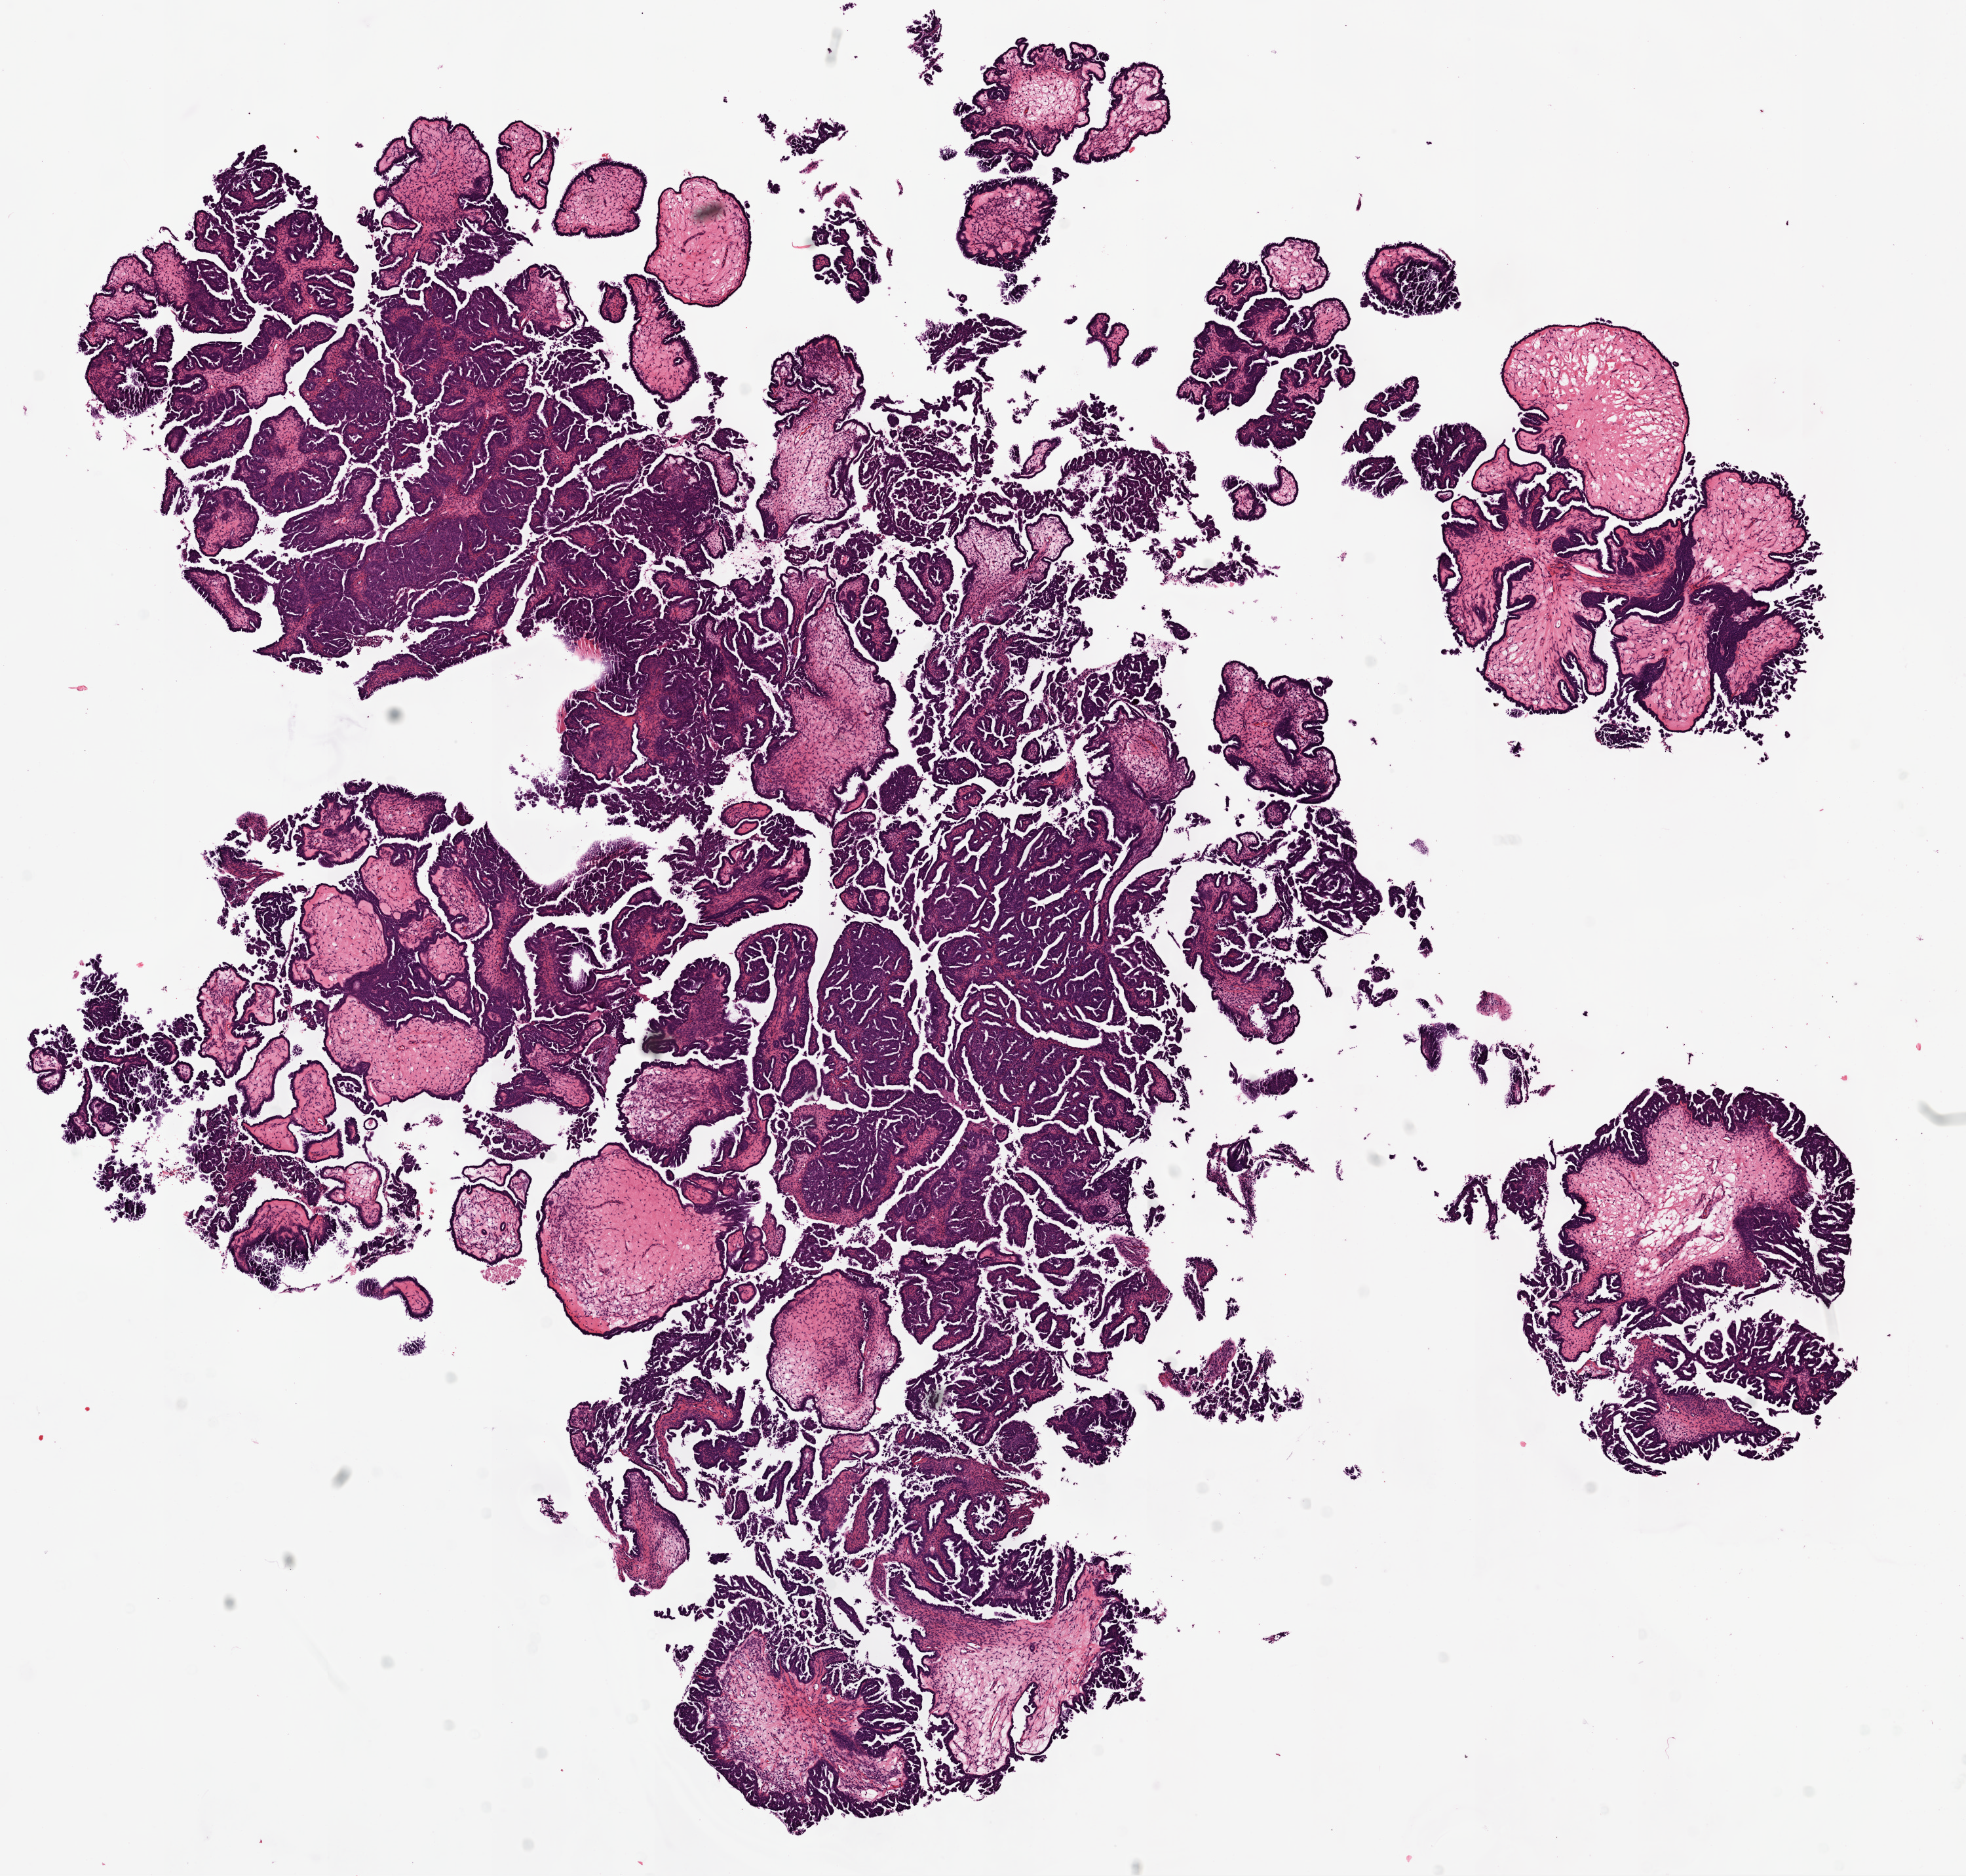
Whole-slide histology image, Hematoxylin and eosin (H&E) stained, a low-resolution overview of the entire scanned area, about 12.0 x 11.5 mm. Frozen section from the top of the tissue portion. Ovary, primary tumour sample. Female, age 39 years at initial diagnosis. Histologic grade: G3 (poorly differentiated). Pathologist review of this section (percent, as recorded): tumour cells 75%, tumour nuclei 70%, normal cells 0%, stromal cells 25%, necrosis 0%.
- FIGO stage: IIIC
- diagnosis: Serous cystadenocarcinoma, NOS
- laterality: bilateral